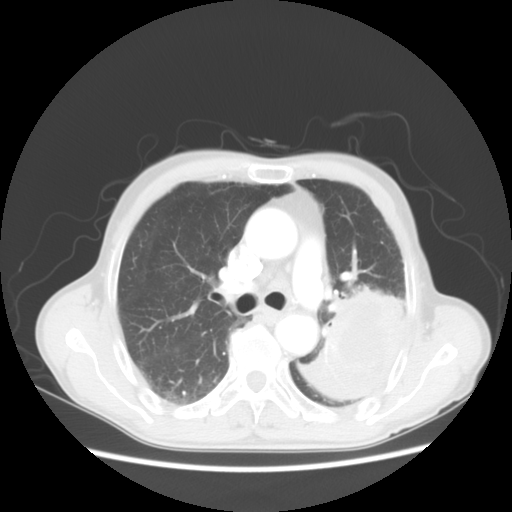
Chest CT, one axial slice. Slice 33 of 51 in the series (ordered by position). 120 kVp. Lung window (W 1500 / L -600 HU). 5 mm slice thickness. 512 × 512 image matrix, field of view 360 × 360 mm. Patient: male, 64 years. Case-level facts recorded for this patient, not image findings: clinical TNM (as recorded): T4 N0 M0; histopathological grade: G2-3.
Annotated regions visible in this slice (bounding box drawn by a radiologist):
- lung tumour (recorded histology: squamous cell carcinoma): bounding box [x1, y1, x2, y2] px = [315, 282, 403, 421]